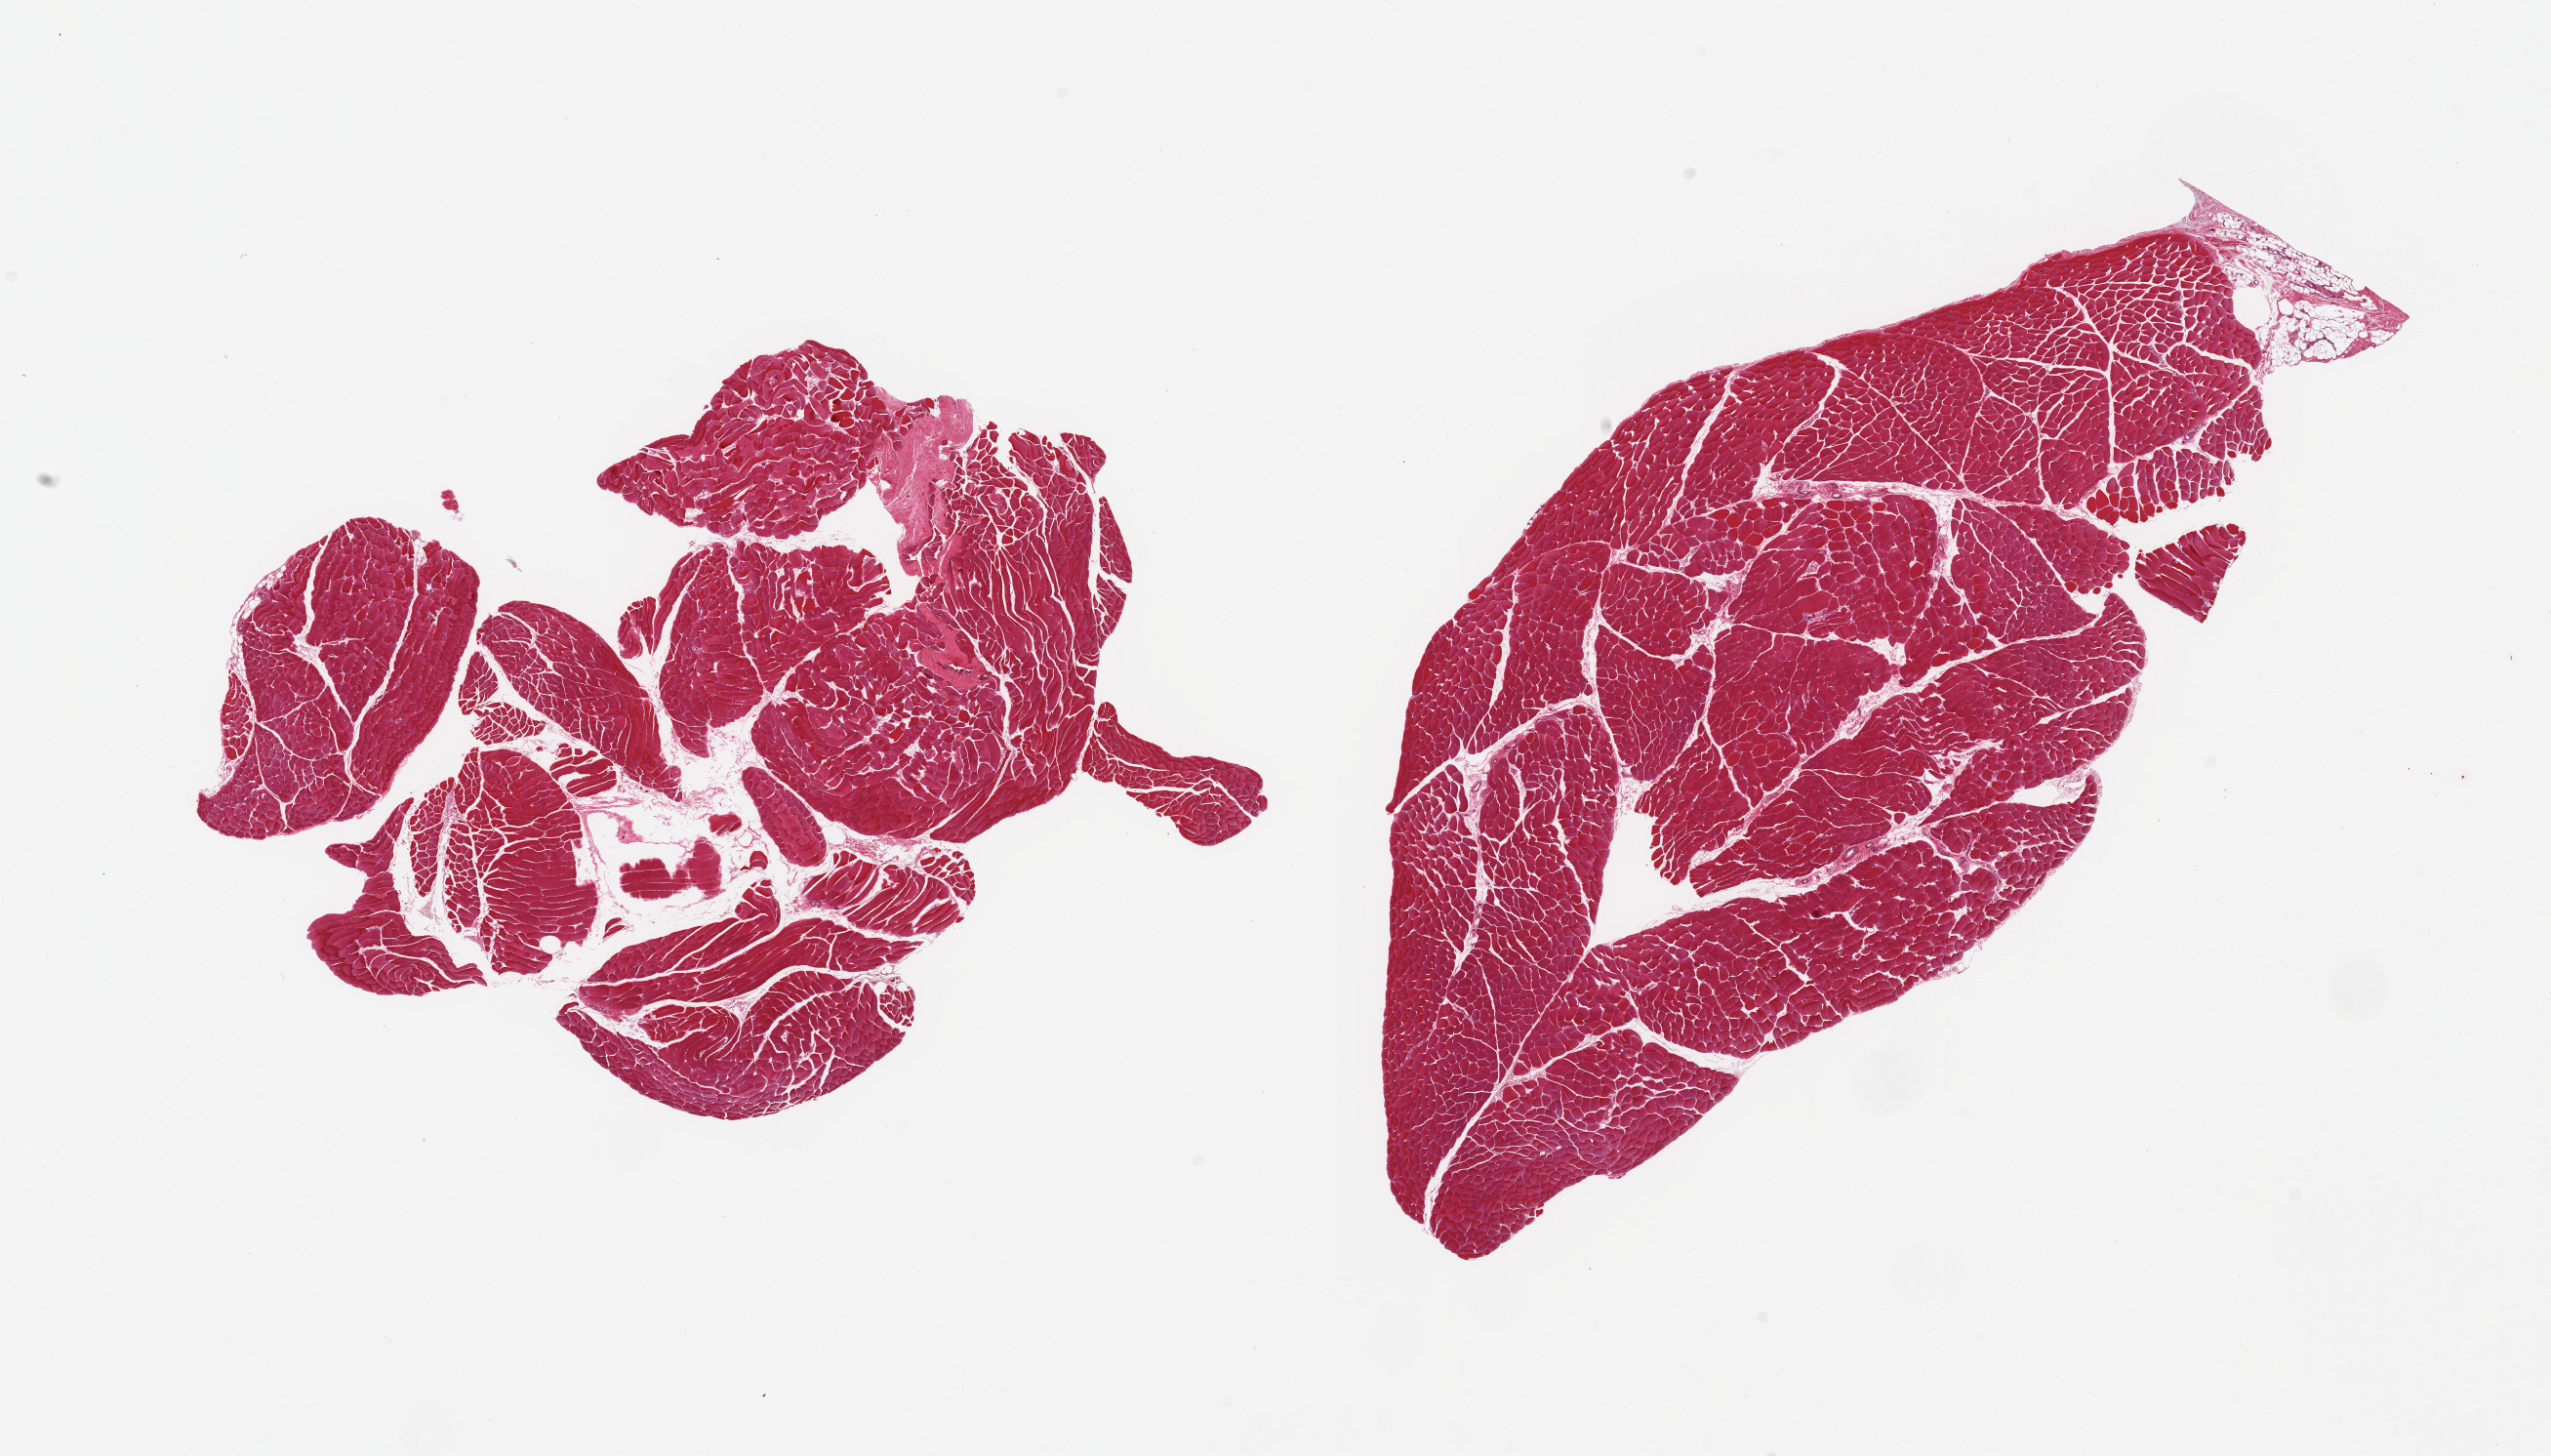
Whole-slide image, H&E stain, low-resolution overview of the scanned area, about 20.7 x 11.8 mm (acquisition: 20x scan); PAXgene-fixed paraffin-embedded (PFPE) section; target tissue: skeletal muscle; donor tissue sample. Female donor.
• pathologist's review note for this sample: 2 pieces, ~5-10% adherent/interstitial fat